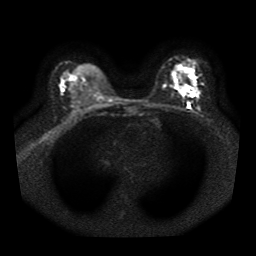
Breast MRI, one axial slice; slice 26 of 41 in the series (ordered by position); diffusion-weighted series; image 2 of 4 stored at this slice position (different b-values; order by instance number); 1.5 T; 5 mm slice thickness; 256 × 256 image matrix, field of view 330 × 330 mm. Female patient.
Structures marked on this image (outlined manually by an expert reader):
- tumour on diffusion-weighted imaging: bounding box <181,87,190,95> (left, top, right, bottom; pixels)